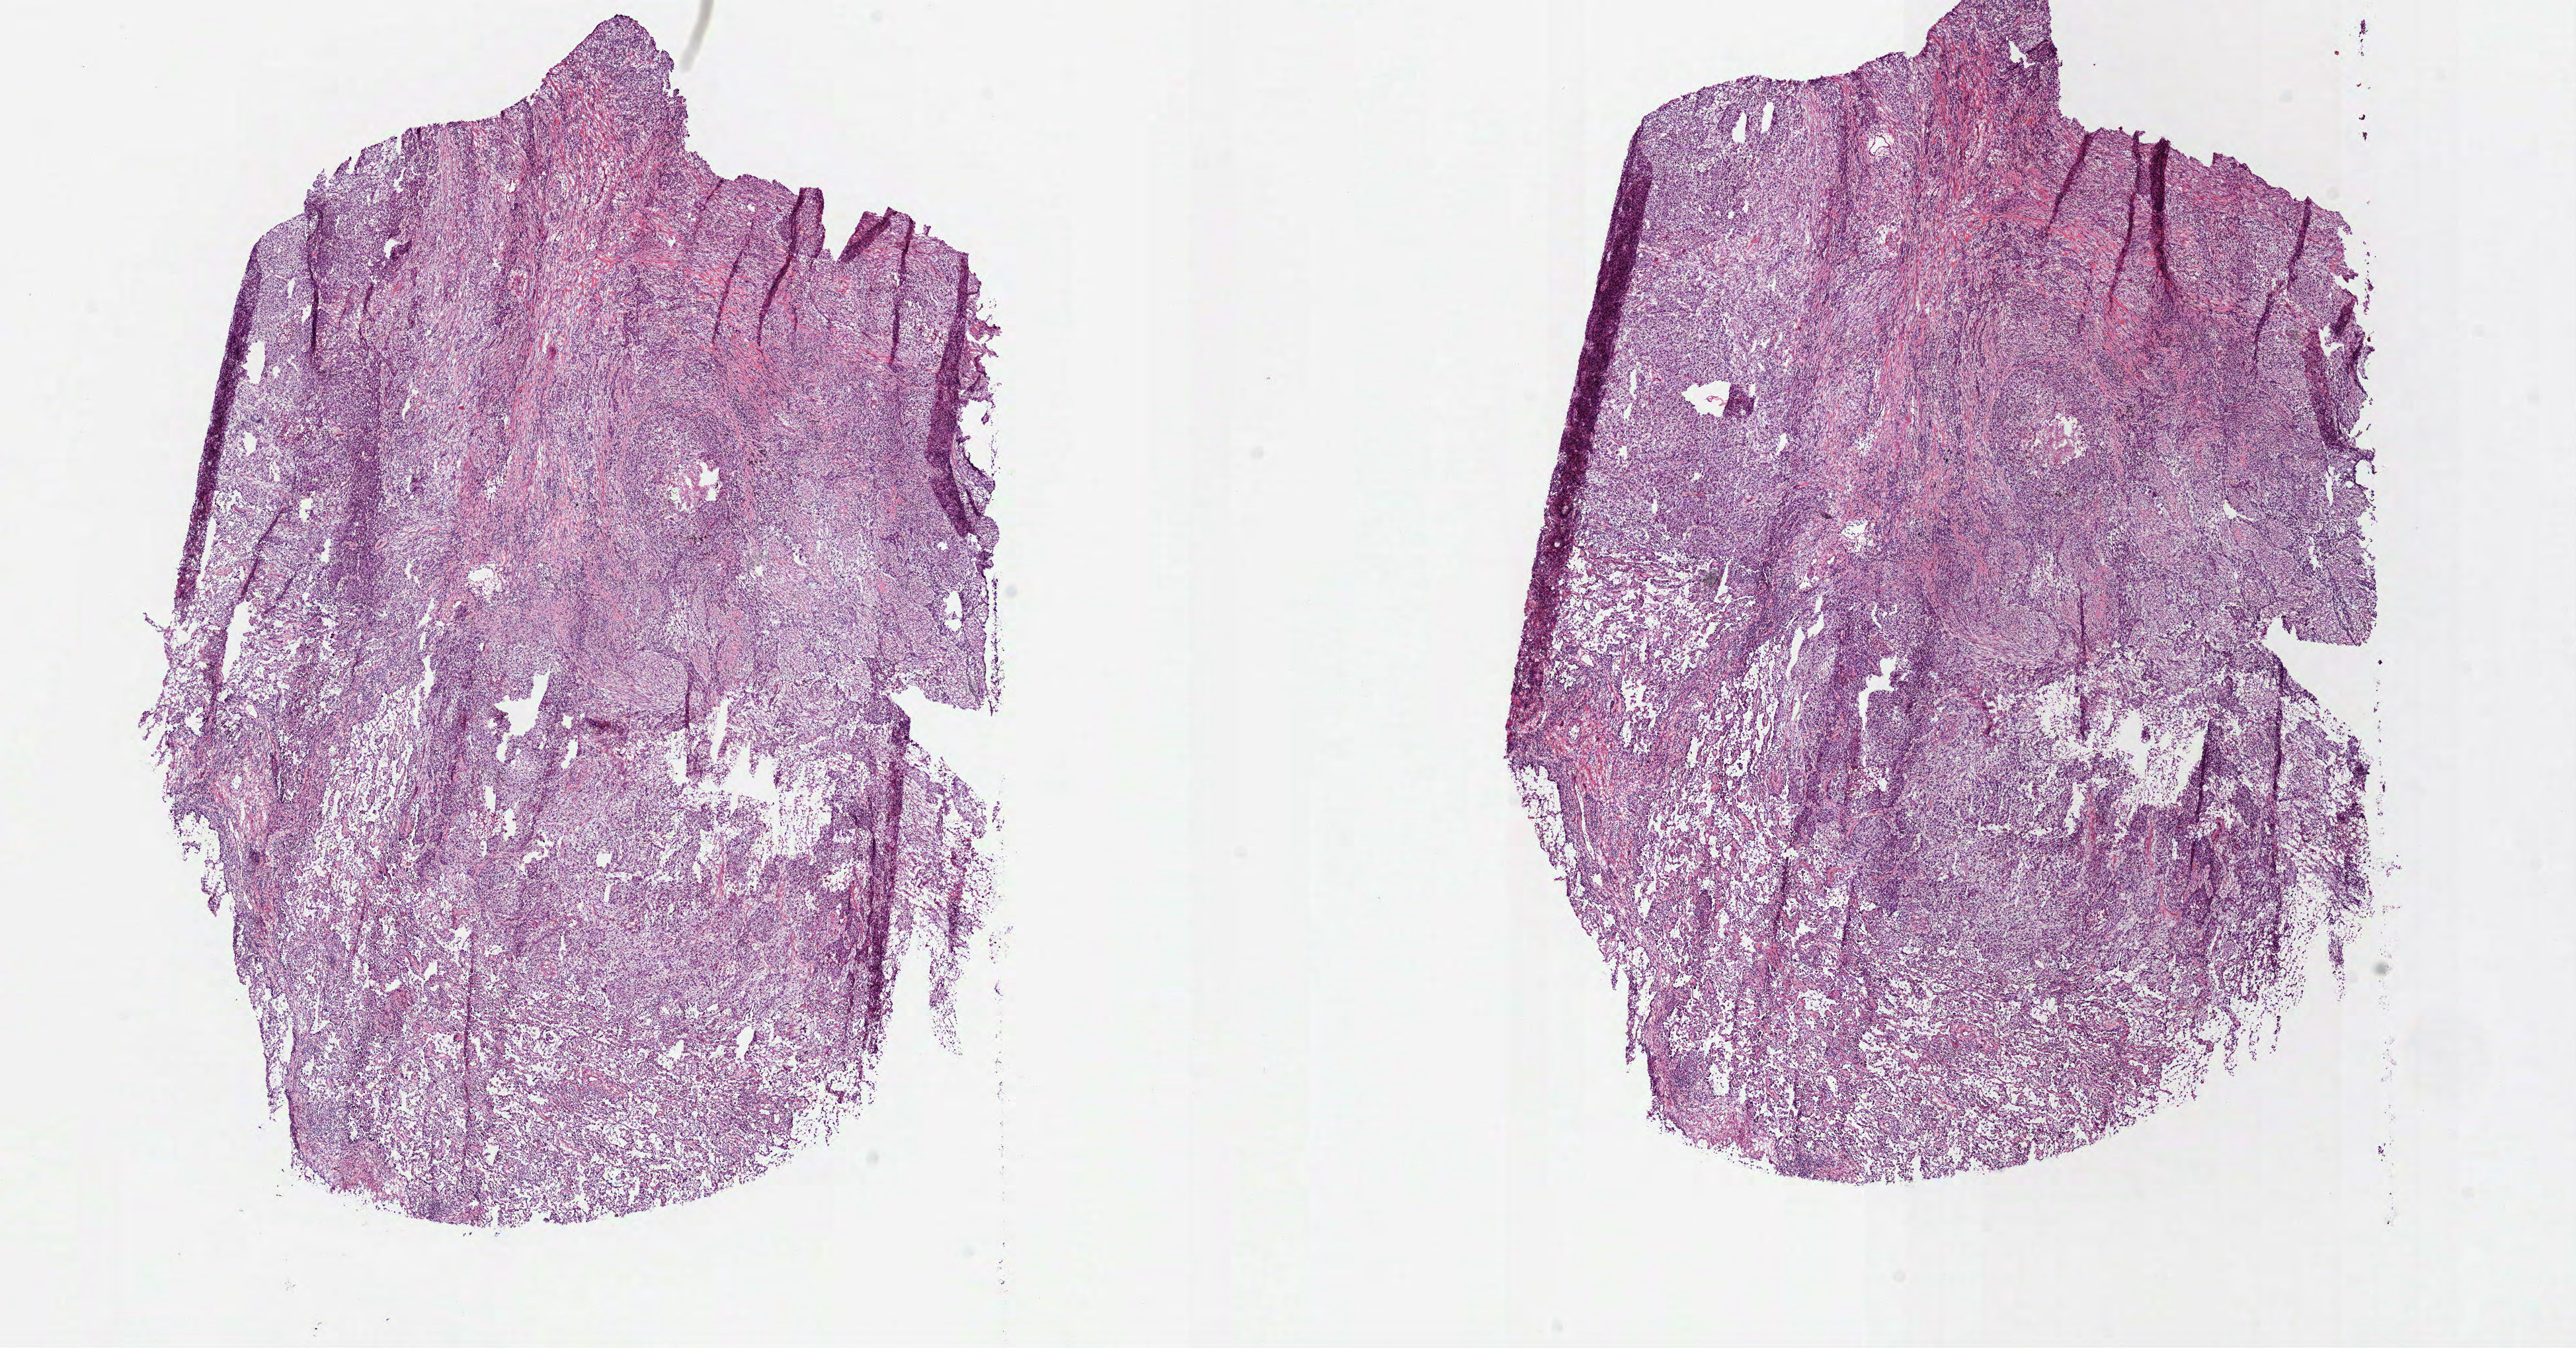
Digitized H&E tissue section (whole slide) — low-resolution overview of the scanned area, about 15.7 x 8.2 mm (from a 40x scan). Frozen section from the top of the tissue portion. Sample: primary tumour, lung. Female patient; age at initial diagnosis 77 years. Slide review estimates, as recorded: tumour cells 65%, tumour nuclei 70%, normal cells 15%, stromal cells 15%, necrosis 5%.
Laterality: right. Pathologic diagnosis: Squamous cell carcinoma, NOS (upper lobe, lung). TNM: T2a N0 M0. AJCC pathologic stage: IB.